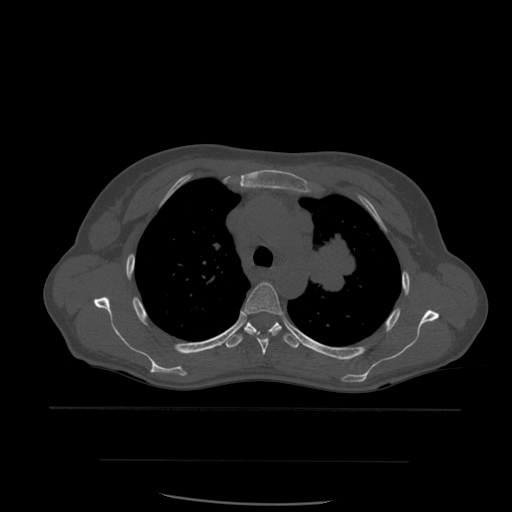
CT including the spine, one axial slice; position 420 of 574 along the scan axis; bone window (W 1800 / L 400 HU); 512 × 512 image matrix, field of view 392 × 392 mm. Patient age 48 years. From the clinical record (not read from this slice): primary cancer: lung.
Annotated regions visible in this slice (semi-automatically segmented with operator editing):
- T4 vertebra: bounding box (x1, y1, x2, y2) in pixels: (242, 282, 282, 356)
- T5 vertebra: (224, 322, 302, 349)